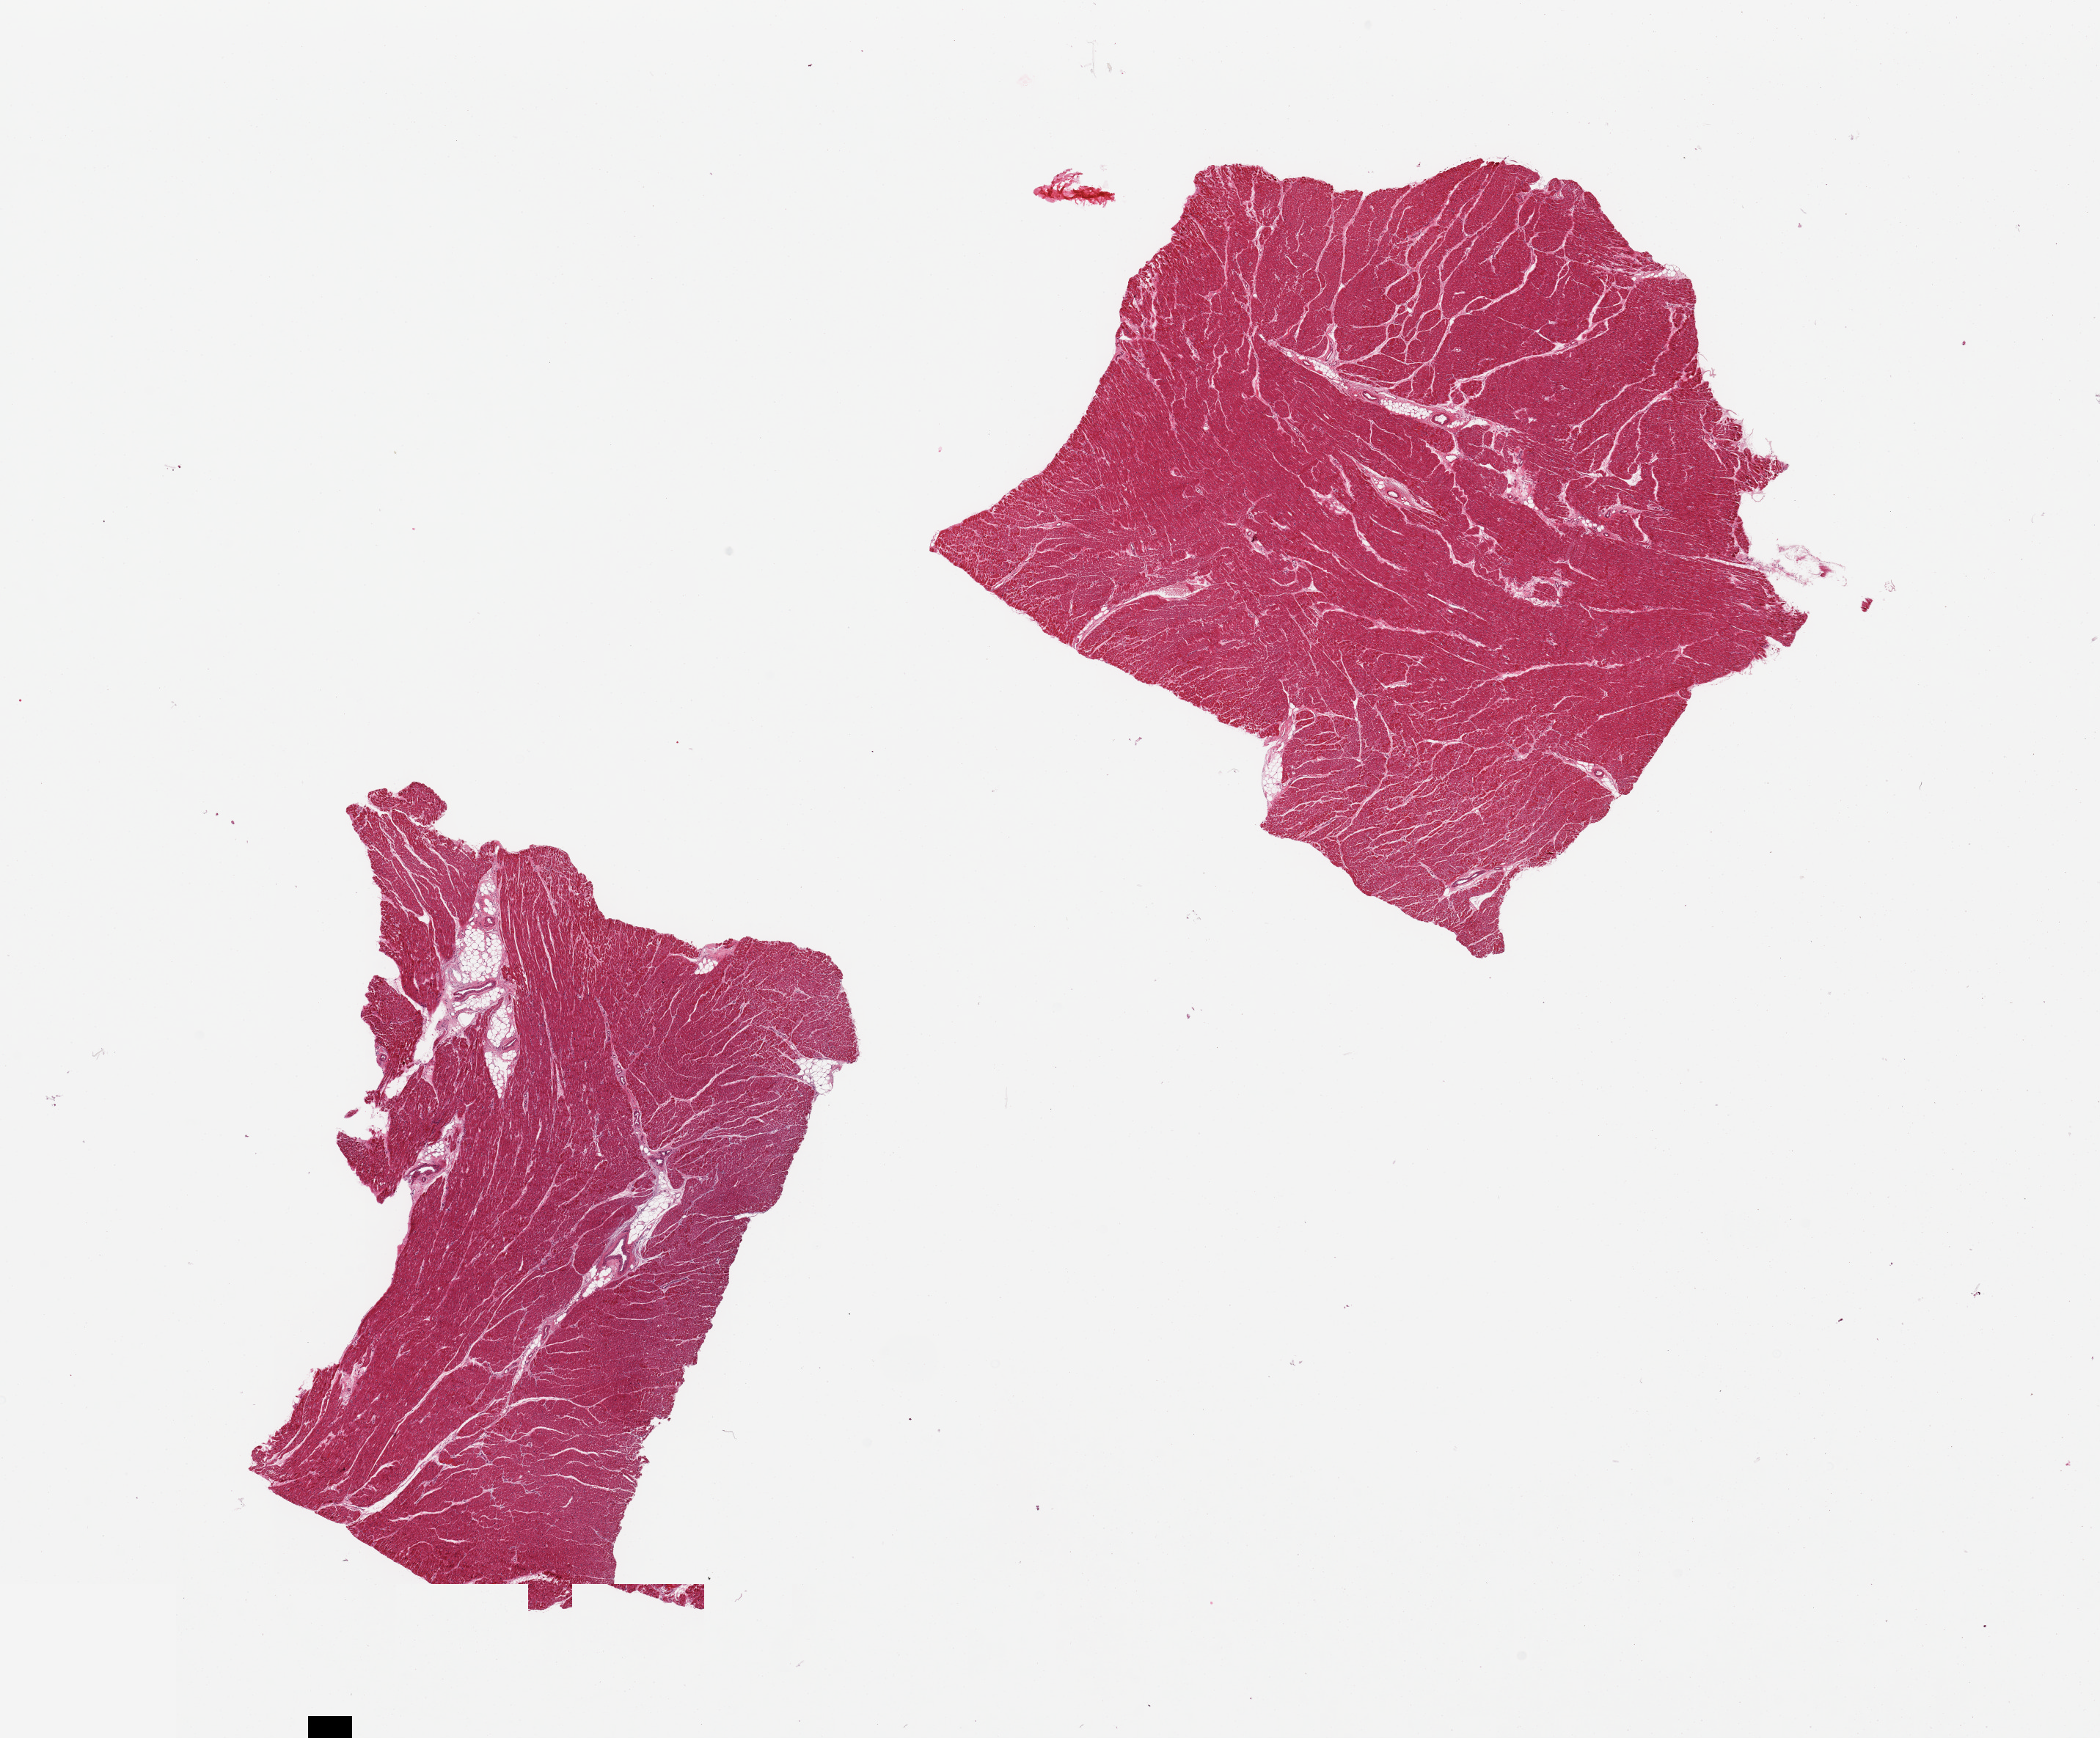
Haematoxylin and eosin whole-slide image — low-resolution overview of the scanned area, about 22.6 x 18.7 mm (acquisition: 20x scan). PAXgene-fixed paraffin-embedded (PFPE) section. Sampled site (target tissue): heart. Donor tissue sample. Donor: female.
Review note (as recorded): 2 pieces; minimal ischemic changes.